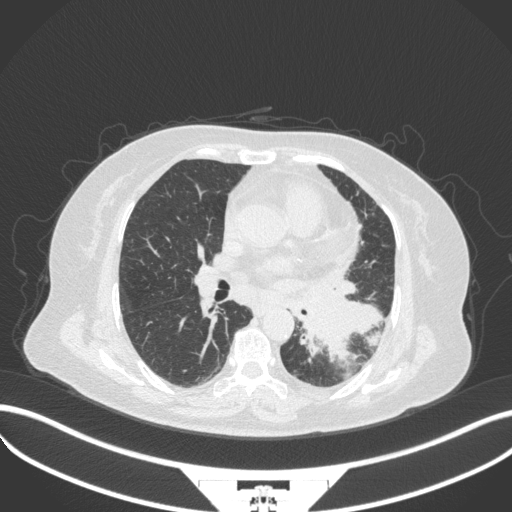
Chest CT, one axial slice. 120 kVp. Lung window (W 1500 / L -600 HU). 1 mm slice thickness. 512 × 512 image matrix, field of view 400 × 400 mm. Female patient, age 69 years. Case-level facts recorded for this patient, not image findings: clinical TNM (as recorded): T2b N3 M1.
Structures marked on this image (rectangle marked by the reading radiologist):
- lung tumour (recorded histology: adenocarcinoma): bounding box <296,290,389,365> (left, top, right, bottom; pixels)